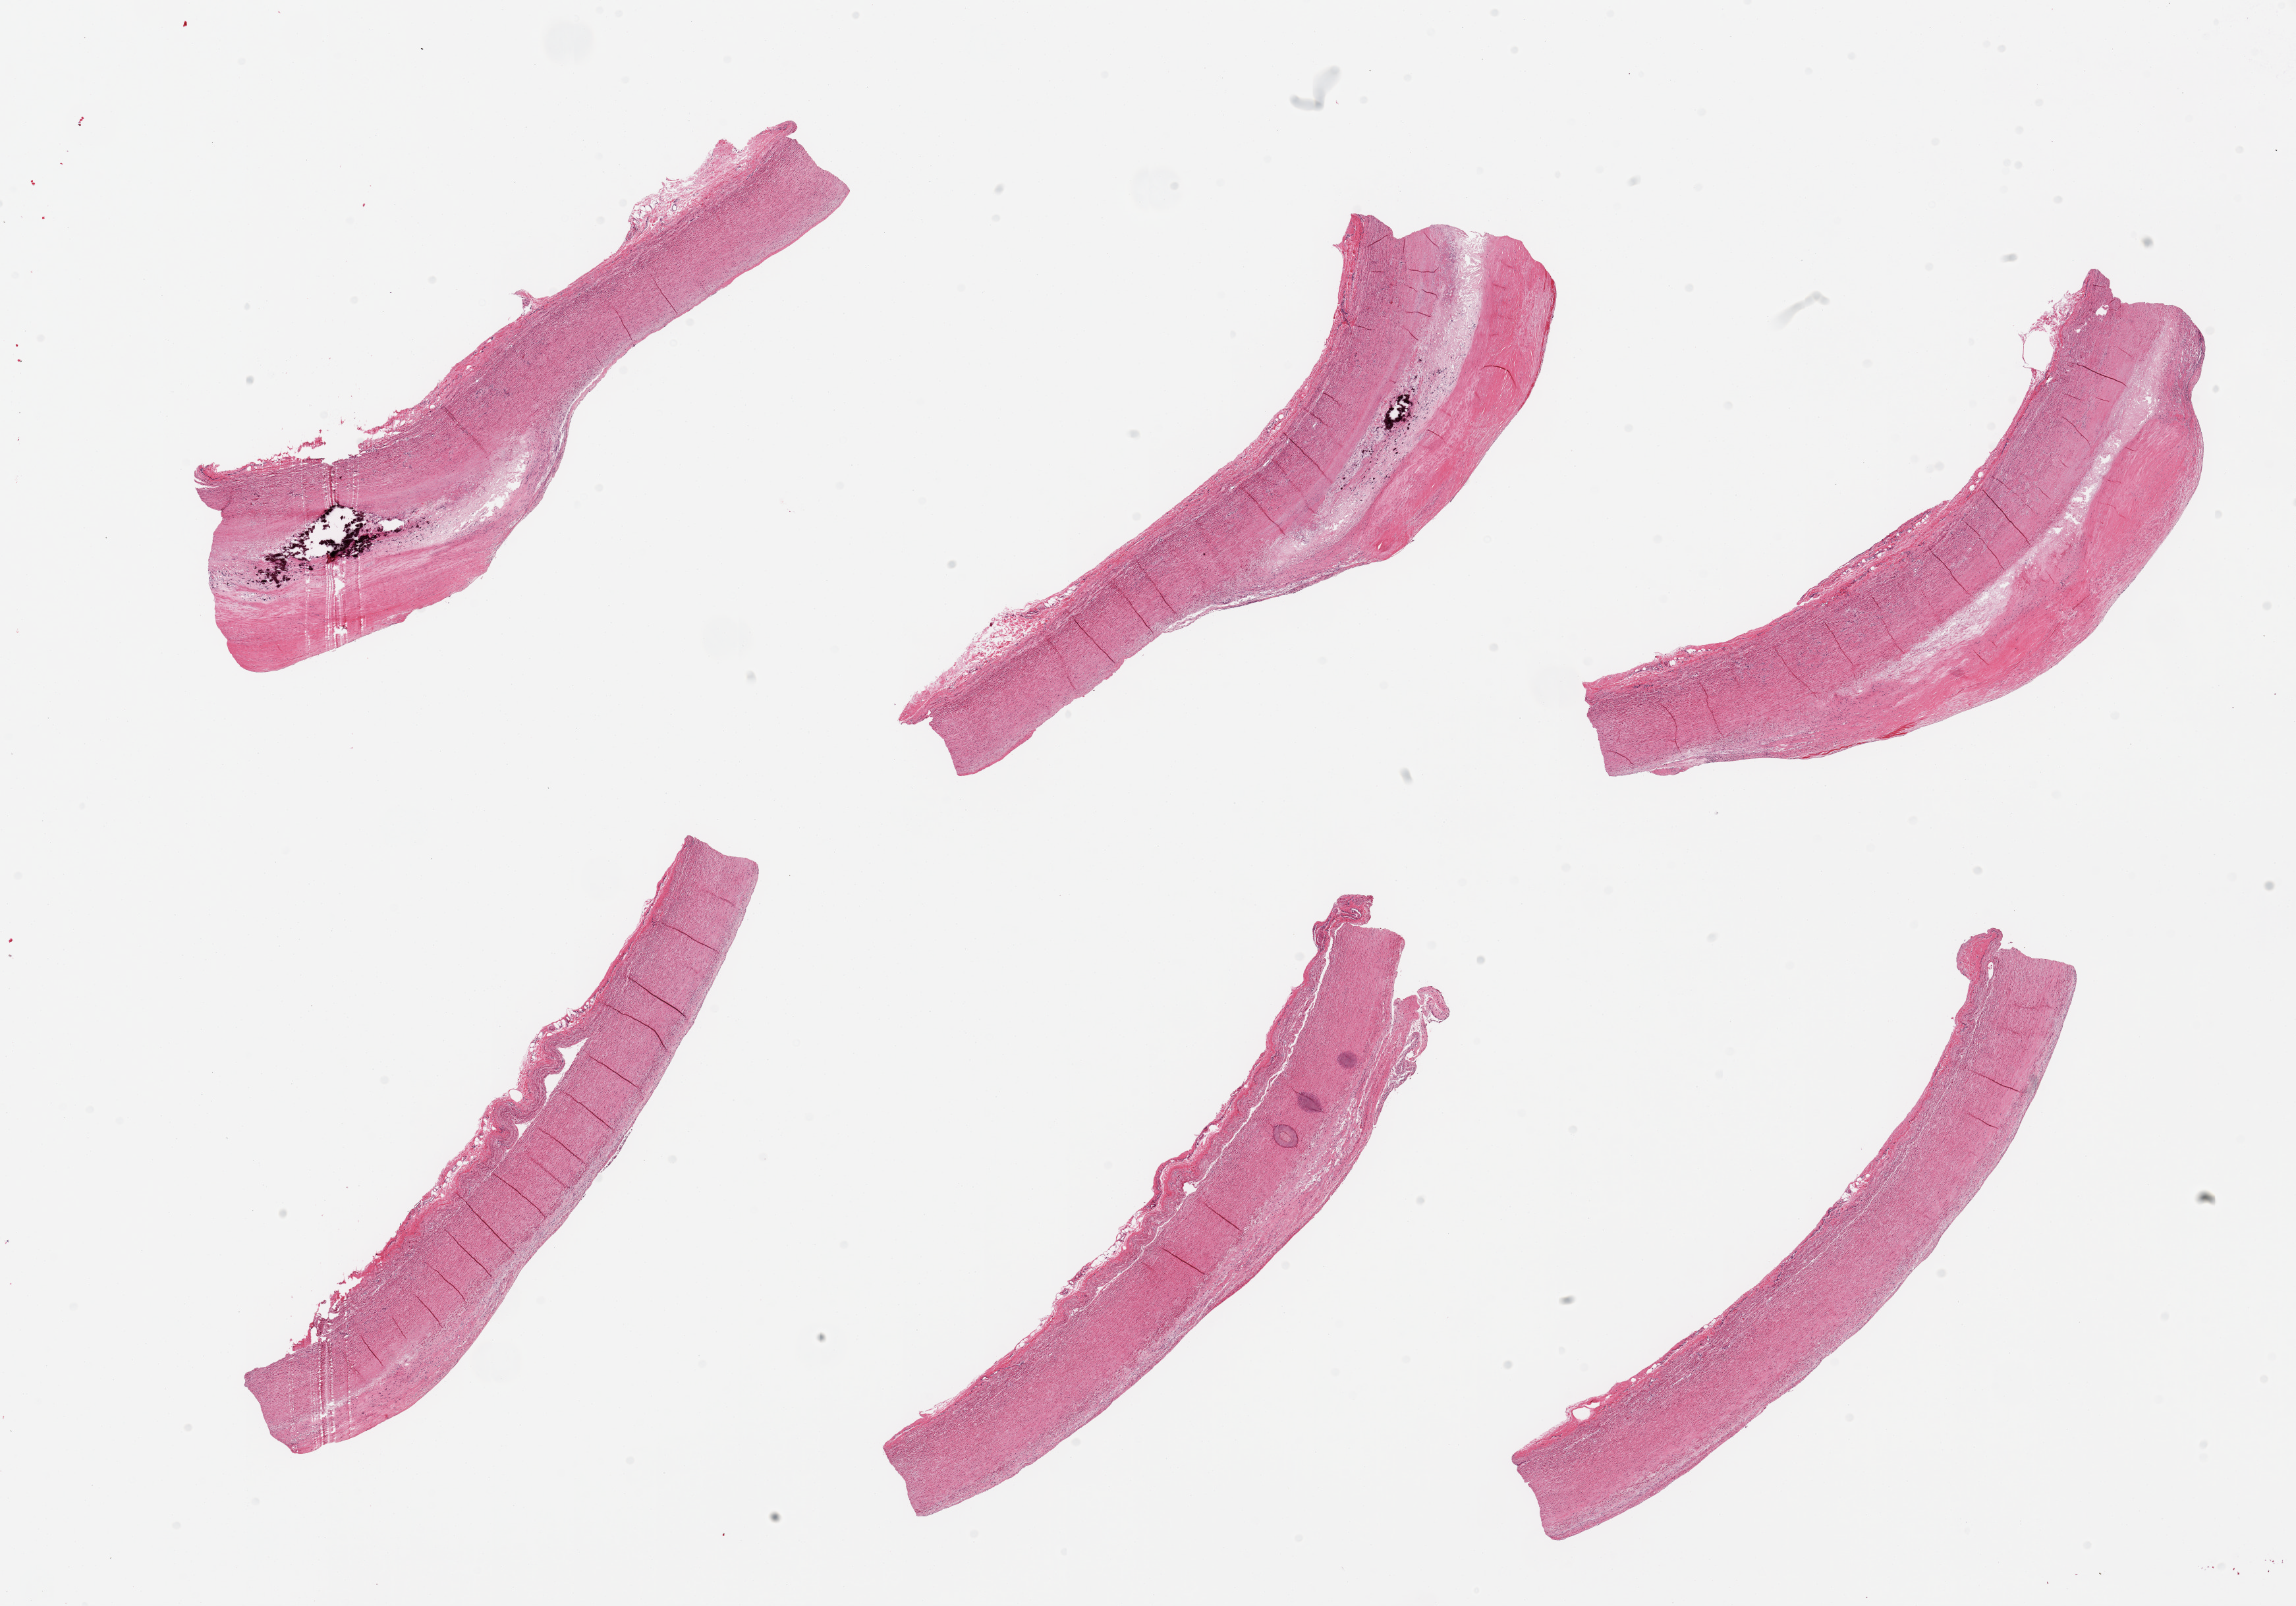
Digitized haematoxylin and eosin-stained section, whole scanned area (about 27.6 x 19.3 mm, from a 20x scan) shown as a low-resolution overview. PAXgene-fixed, paraffin-embedded tissue. Section of aorta (target tissue). Tissue donor sample. Female donor.
Pathologist's review note for this sample: 6 pieces; calcified atherosclerotic plaques.